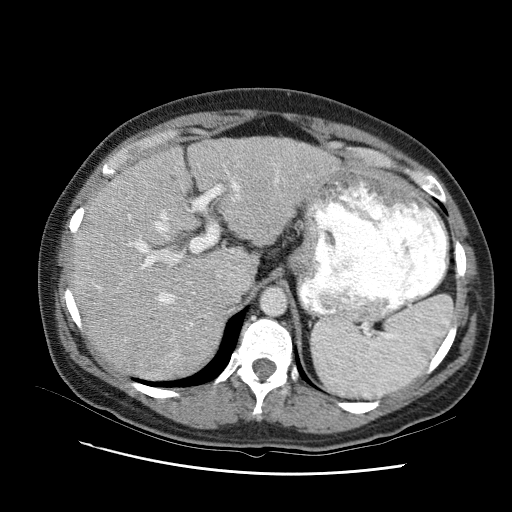
Contrast-enhanced abdominal CT (liver protocol), one axial slice; slice 67 of 95 in the series (ordered by position); reconstruction kernel STANDARD; one of 2 acquisitions stored at this slice position; soft-tissue window (W 400 / L 40 HU); 512 × 512 image matrix, field of view 360 × 360 mm. From the clinical record (not read from this slice): diagnosis: hepatocellular carcinoma (patient treated with transarterial chemoembolisation; whether this scan precedes or follows treatment is not stated here); TNM stage (as recorded): Stage-I; Child-Pugh class: B.
Annotated regions visible in this slice (semi-automatically segmented with operator editing):
- liver parenchyma outside the tumour (the mass and vessels are separate outlines, so this box may not span the whole liver): bounding box (x1, y1, x2, y2) in pixels: (68, 134, 341, 366)
- liver vessels: (98, 159, 278, 344)